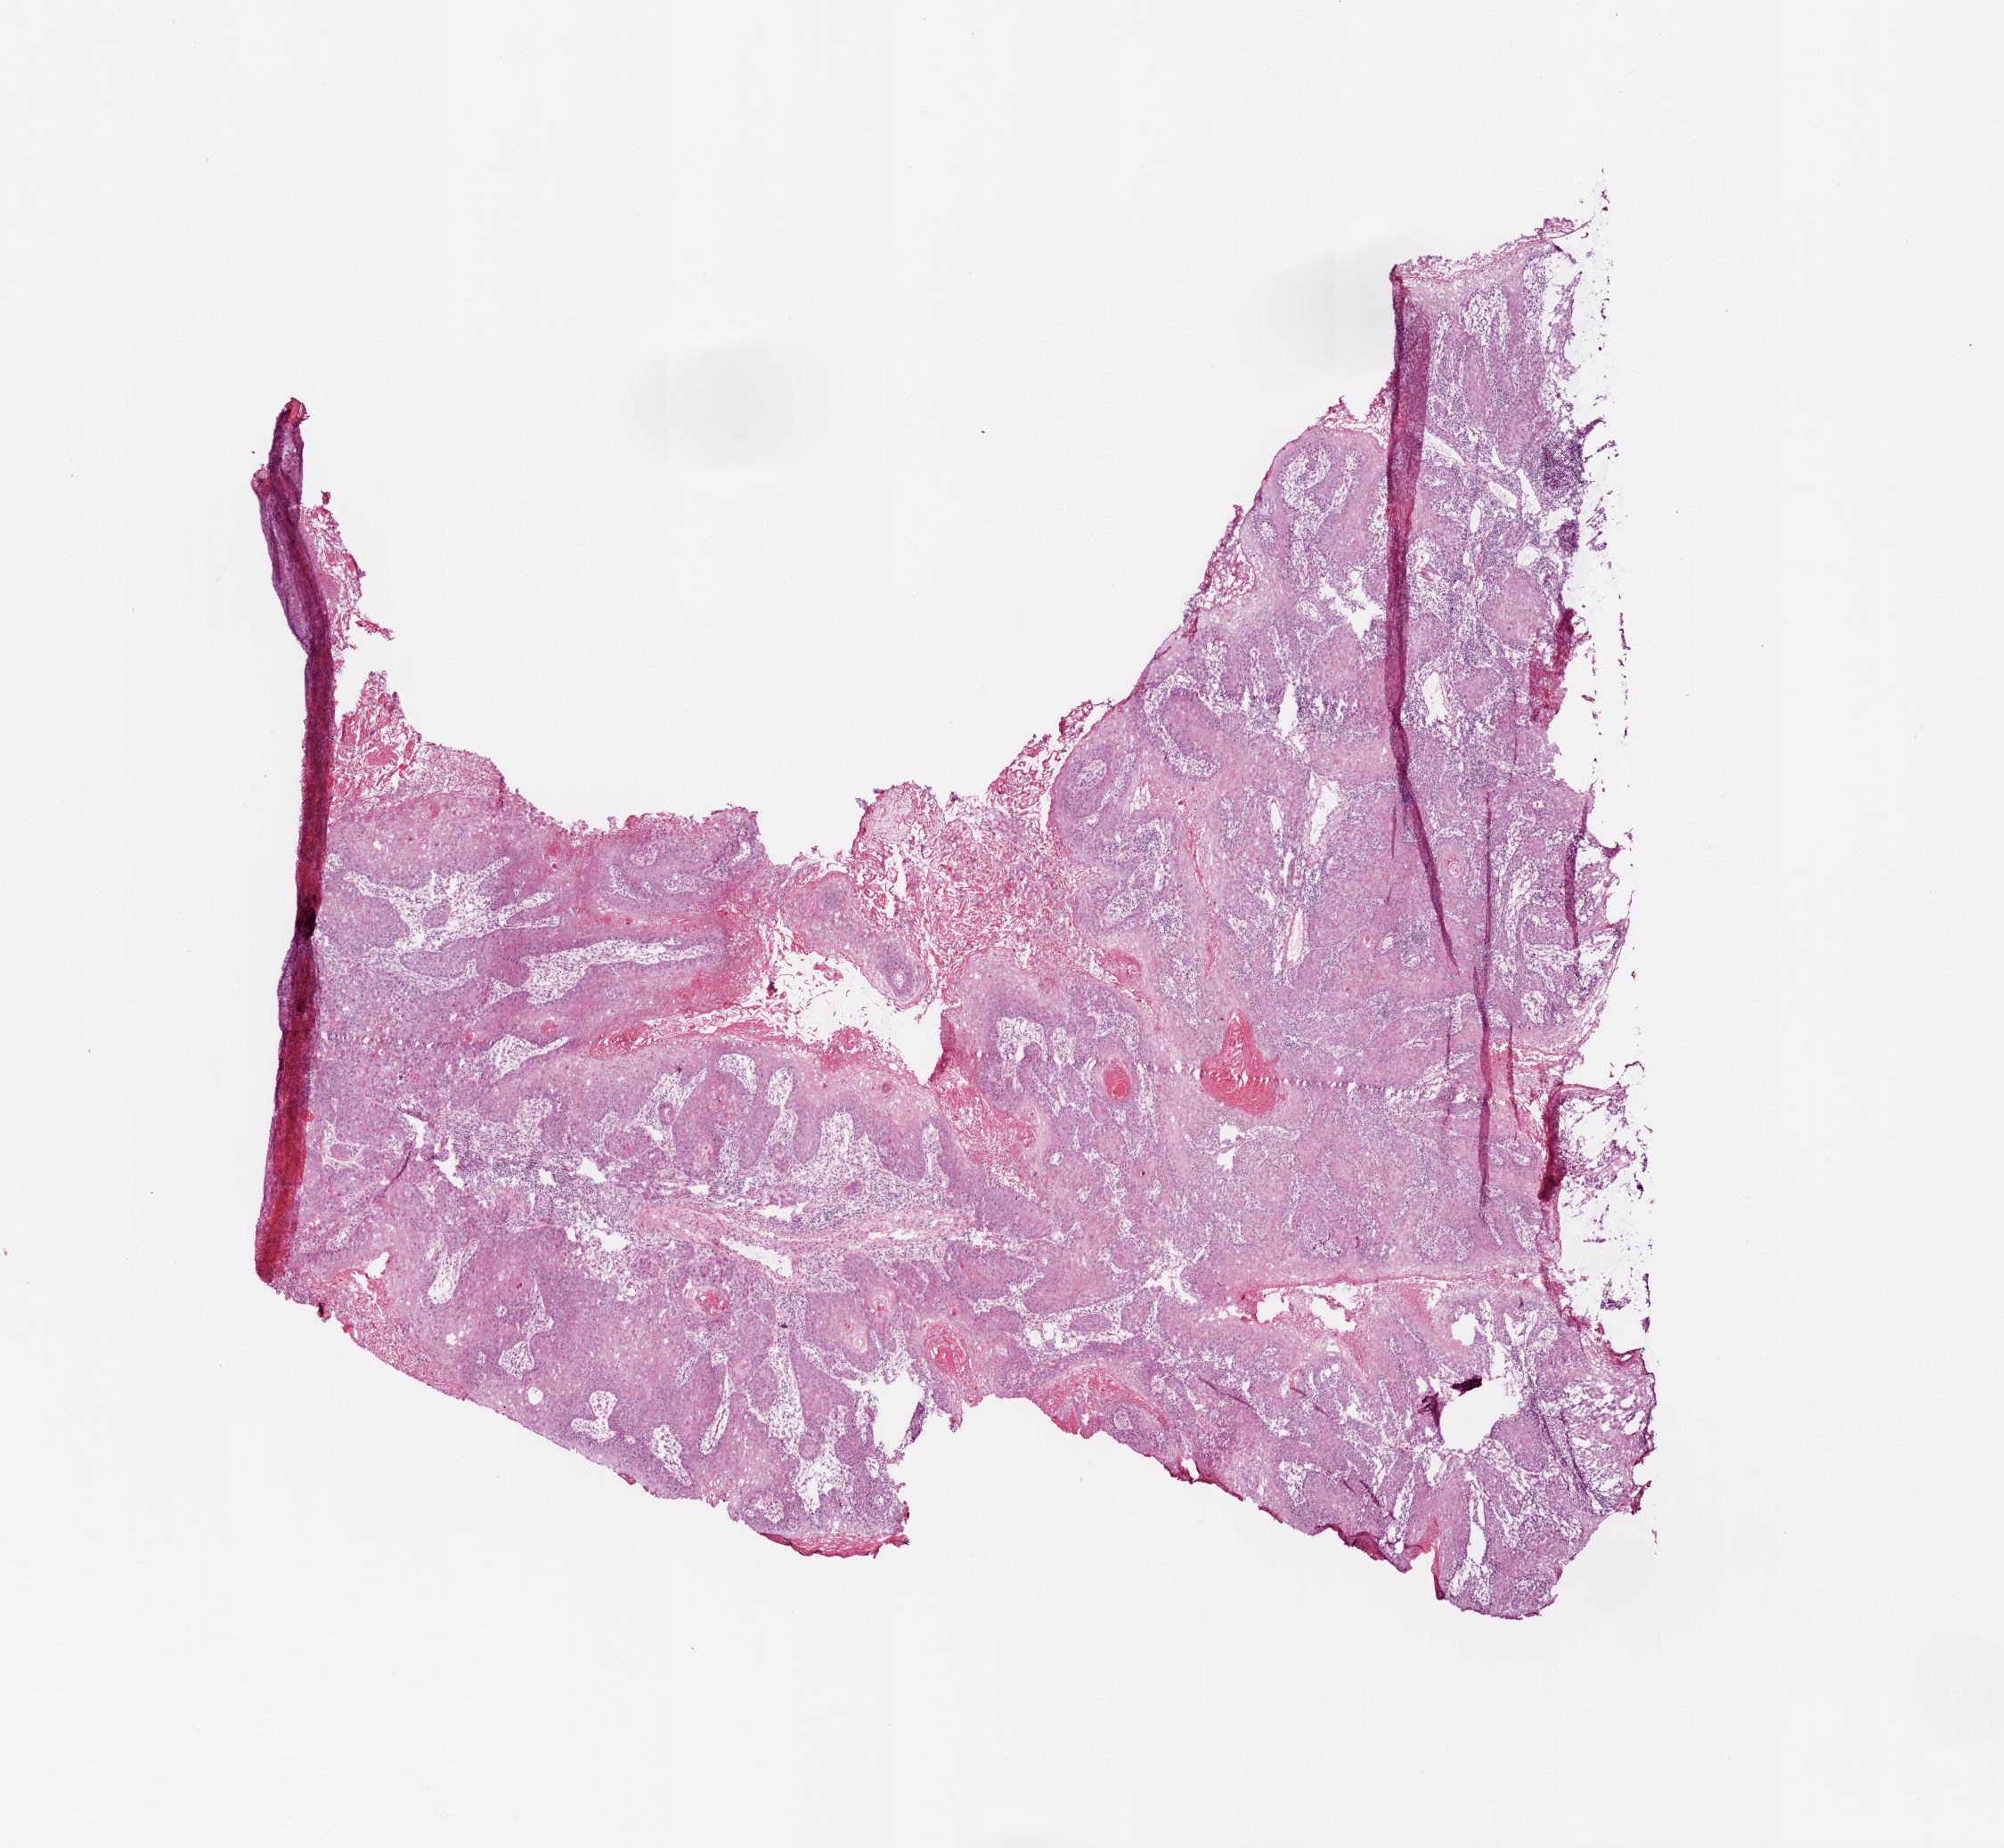
Whole-slide histology image, H&E, low-resolution overview of the scanned area, about 9.0 x 8.3 mm (slide scanned at 20x), frozen section, primary tumour sample from the head and neck. Patient: male, age at initial diagnosis 72 years. Histologic grade: G1 (well differentiated). Slide review estimates, as recorded: tumour cells 85%, tumour nuclei 70%, normal cells 0%, stromal cells 15%, necrosis 0%.
* laterality: left
* pathologic diagnosis: Squamous cell carcinoma, NOS (cheek mucosa)
* AJCC pathologic stage: IVA (7th edition)